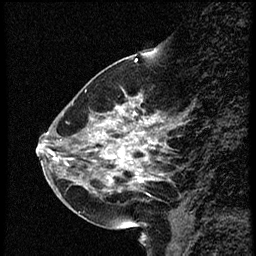
Breast MRI (dynamic contrast-enhanced), one sagittal slice. Position 18 of 56 along the scan axis. Dynamic contrast-enhanced study with each time point stored as its own series, time point 2 of 4 at this slice position (early post-contrast, ordered by acquisition time). 1.5 T. TE 4.2 ms, TR 18.9 ms. 2 mm slice thickness. 256 × 256 image matrix. Female patient. Case-level facts recorded for this patient, not image findings: setting: breast cancer imaged before/during neoadjuvant chemotherapy; receptor status: HER2-positive.
Structures marked on this image (semi-automatically segmented with operator editing):
- analysis volume of interest (the breast-tissue region the enhancement analysis was run in; not a lesion): box from (x=63, y=80) to (x=167, y=215) px
- tumour enhancement mask (voxels above the 100 % enhancement threshold inside the analysis volume of interest): (x=92, y=96)–(x=159, y=185)